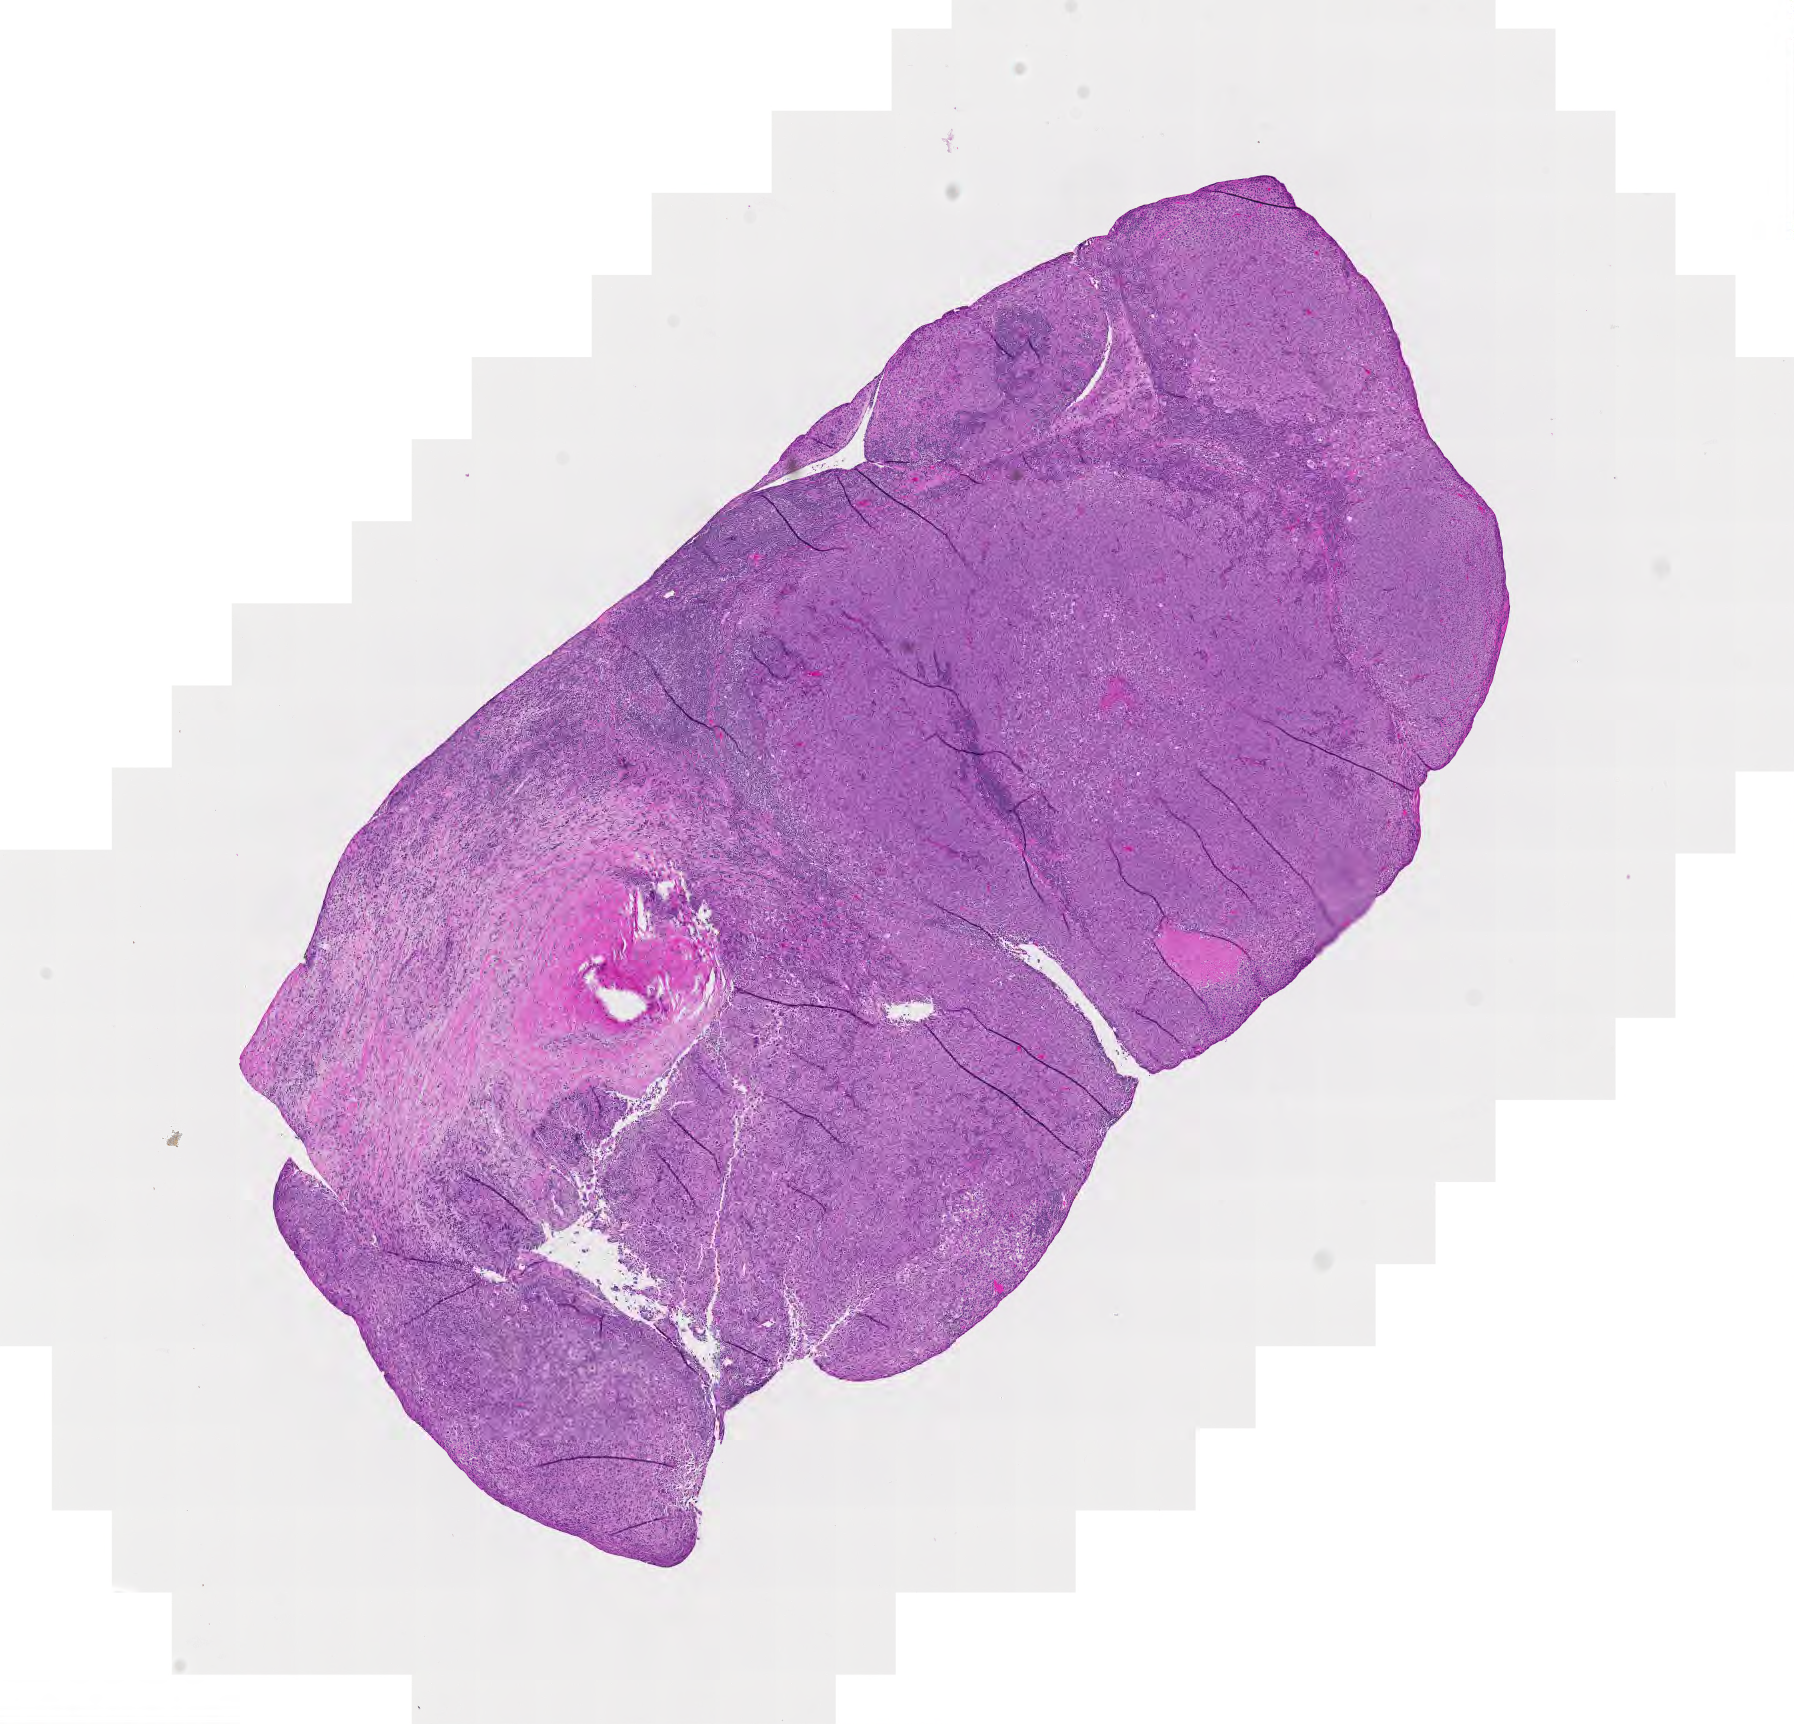
Whole-slide histology image, H&E, whole scanned area (about 9.3 x 8.9 mm) shown as a low-resolution overview; tumour tissue sample, sampled site: lymph node. Male, 68 y/o. Slide review estimates, as recorded: tumour nuclei 80%, necrosis 5%.
This section: metastatic tumour tissue. Patient diagnosis: Malignant melanoma, NOS.